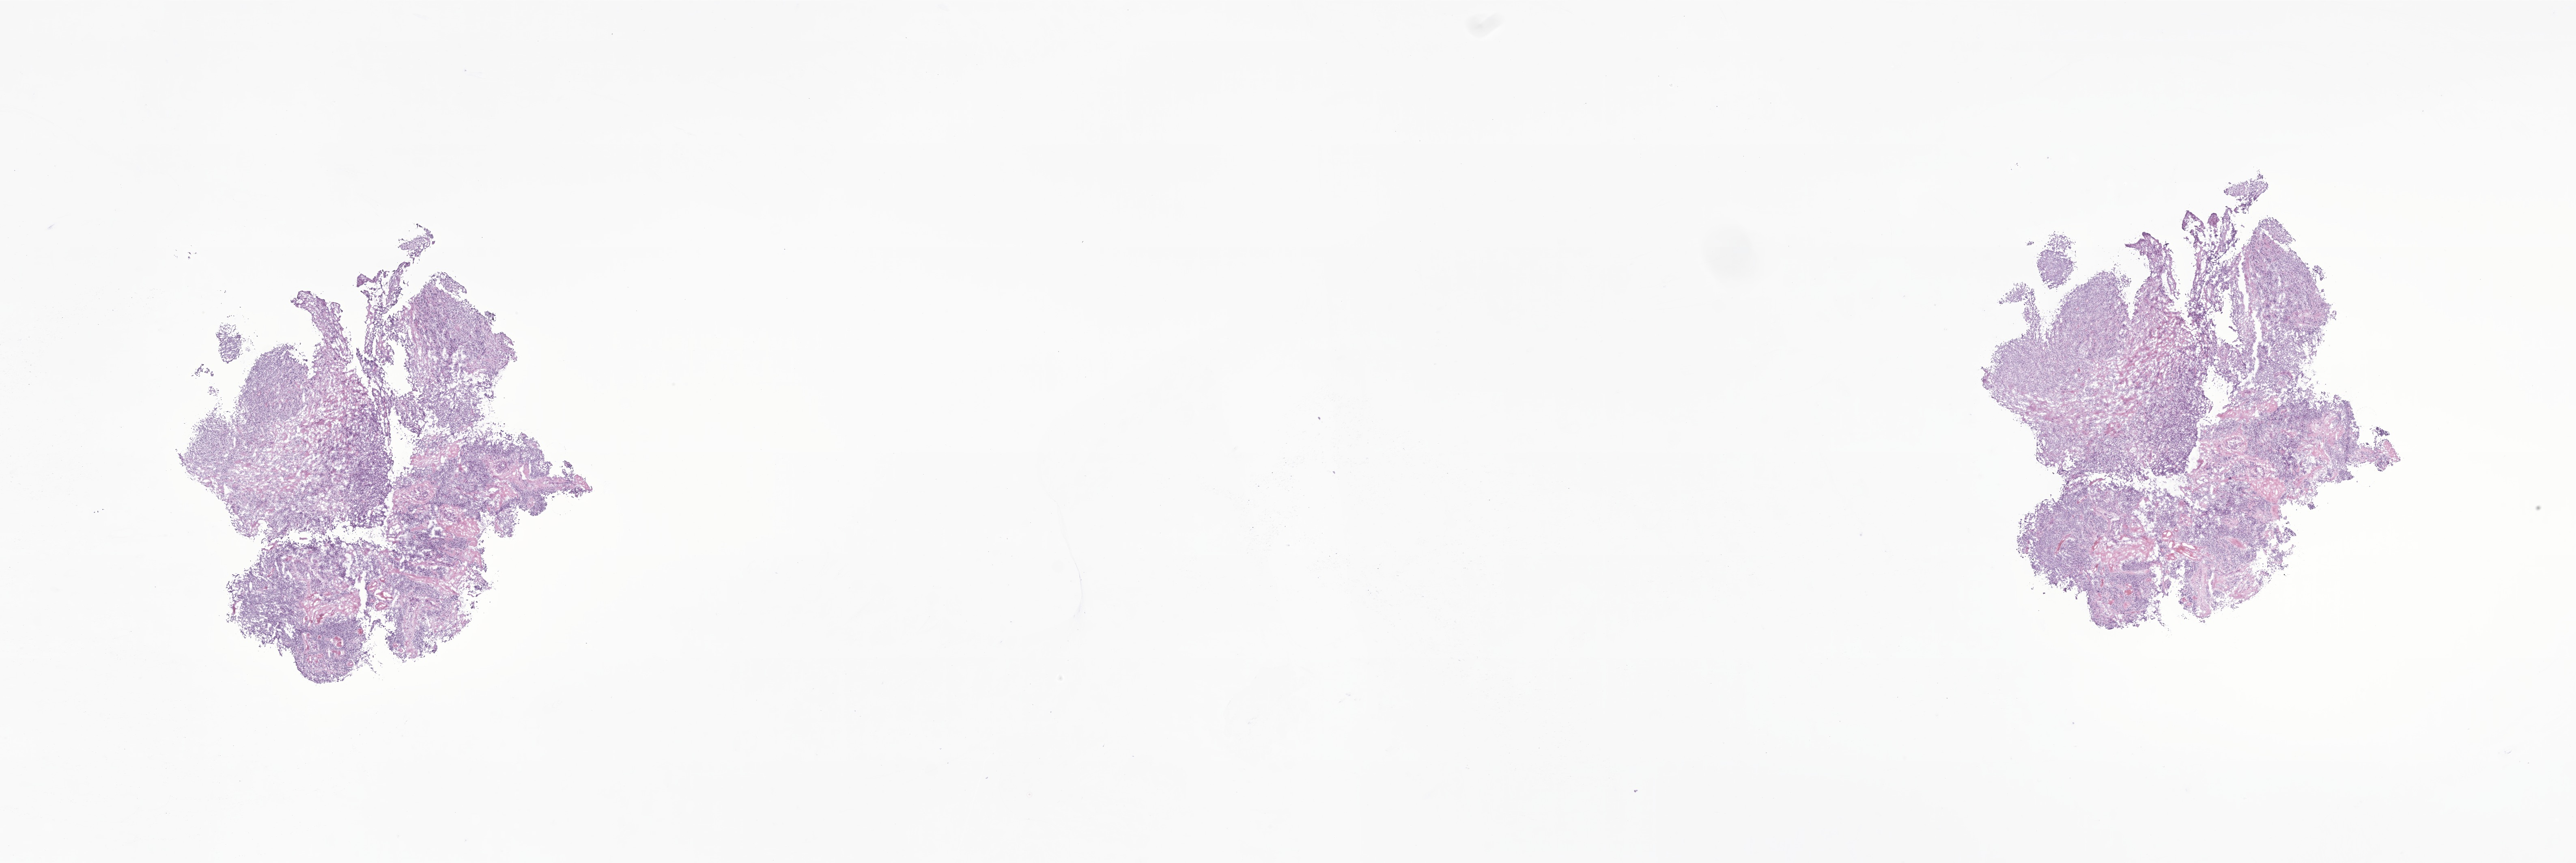
Hematoxylin and eosin (H&E) whole-slide image of tumor tissue from the soft tissue — a low-resolution overview of the entire scanned area, about 26.8 x 9.0 mm, cryosection (OCT / tissue freezing medium). Male patient, age 213 months (17 years 9 months).
Recorded diagnosis: Ewing sarcoma.